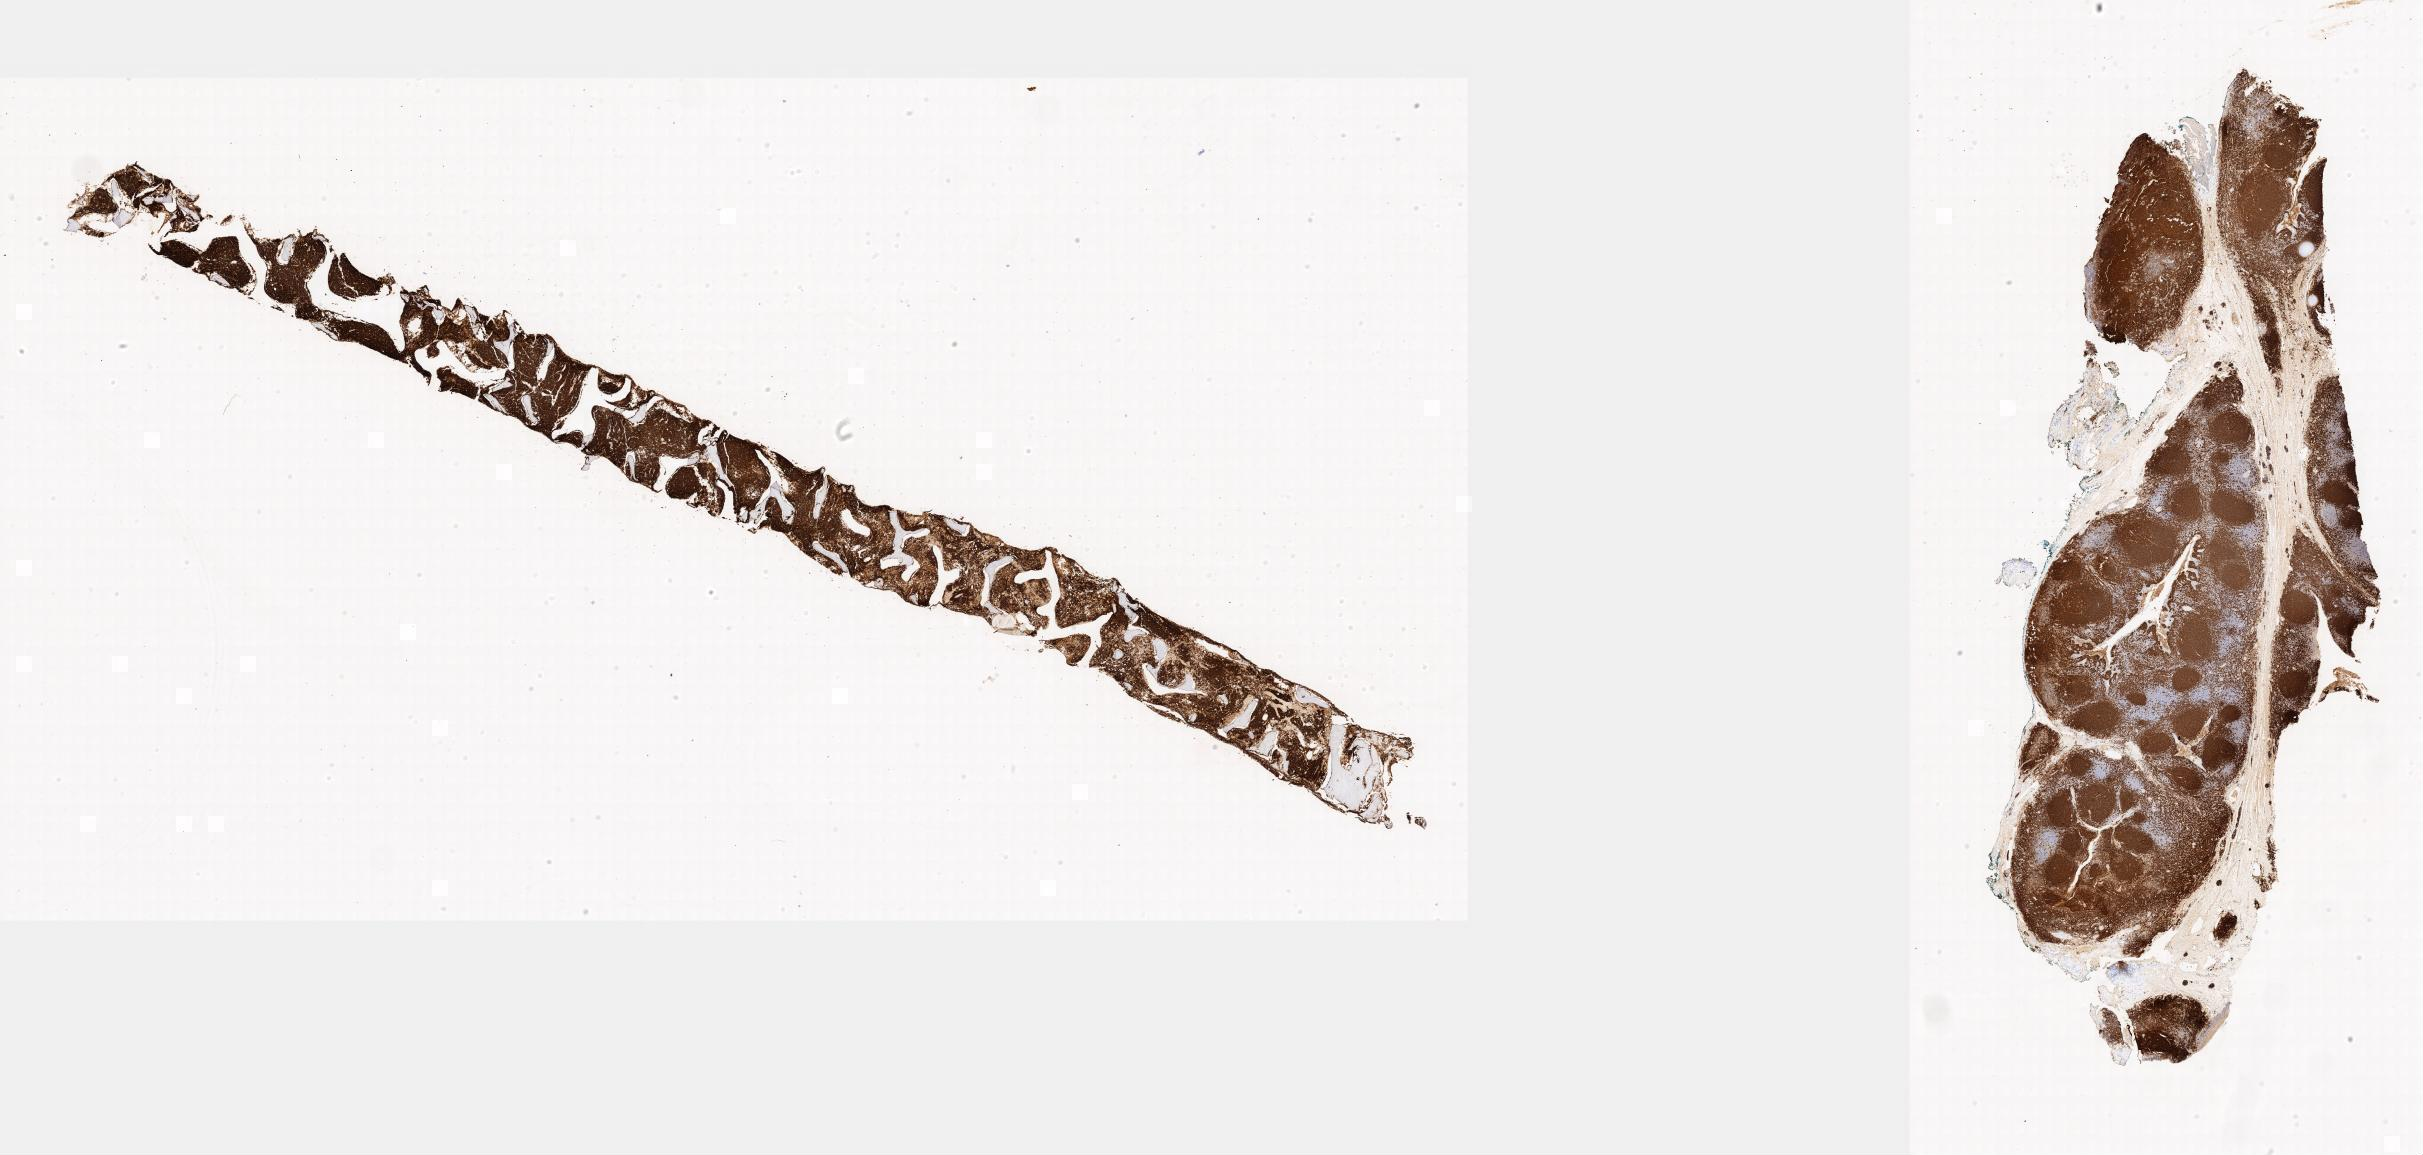
IHC for CD20, whole-slide image — whole scanned area shown as a low-resolution overview; tumor tissue; anatomic site: bone marrow. Male patient, age 18 years.
Histologic diagnosis: Burkitt lymphoma, NOS.